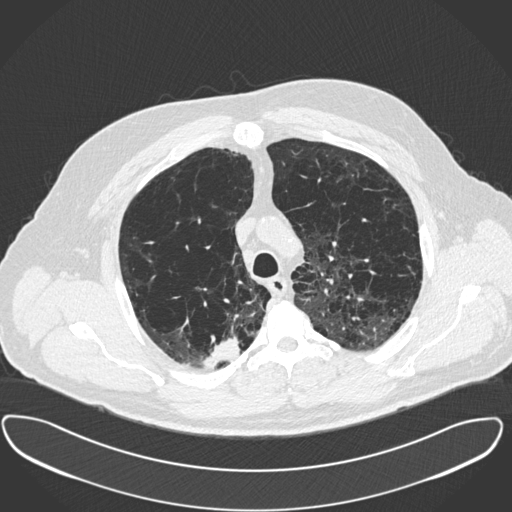
Low-dose screening chest CT, one axial slice. Slice 298 of 385 in the series (ordered by position). 120 kVp. Lung window (W 1500 / L -600 HU). 1 mm slice thickness. 512 × 512 image matrix, field of view 408 × 408 mm.
Annotated regions visible in this slice (outlined manually by an expert reader):
- lesion 1 (tumor, upper lobe of right lung): bounding box [x1, y1, x2, y2] px = [203, 337, 240, 369]